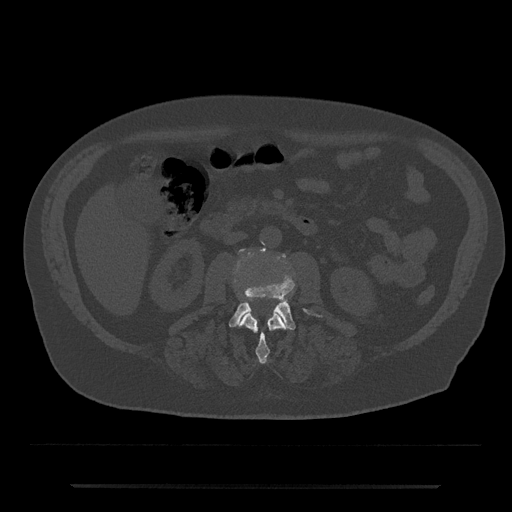
CT including the spine, one axial slice; slice 437 of 797 in the series (ordered by position); bone window (W 1800 / L 400 HU); 512 × 512 image matrix. Patient: male, 80 years. From the clinical record (not read from this slice): primary cancer: prostate.
Annotated regions visible in this slice (semi-automatic segmentation, software-assisted and operator-edited):
- L2 vertebra: box from (x=239, y=310) to (x=287, y=364) px
- L3 vertebra: (x=229, y=248)–(x=322, y=330)